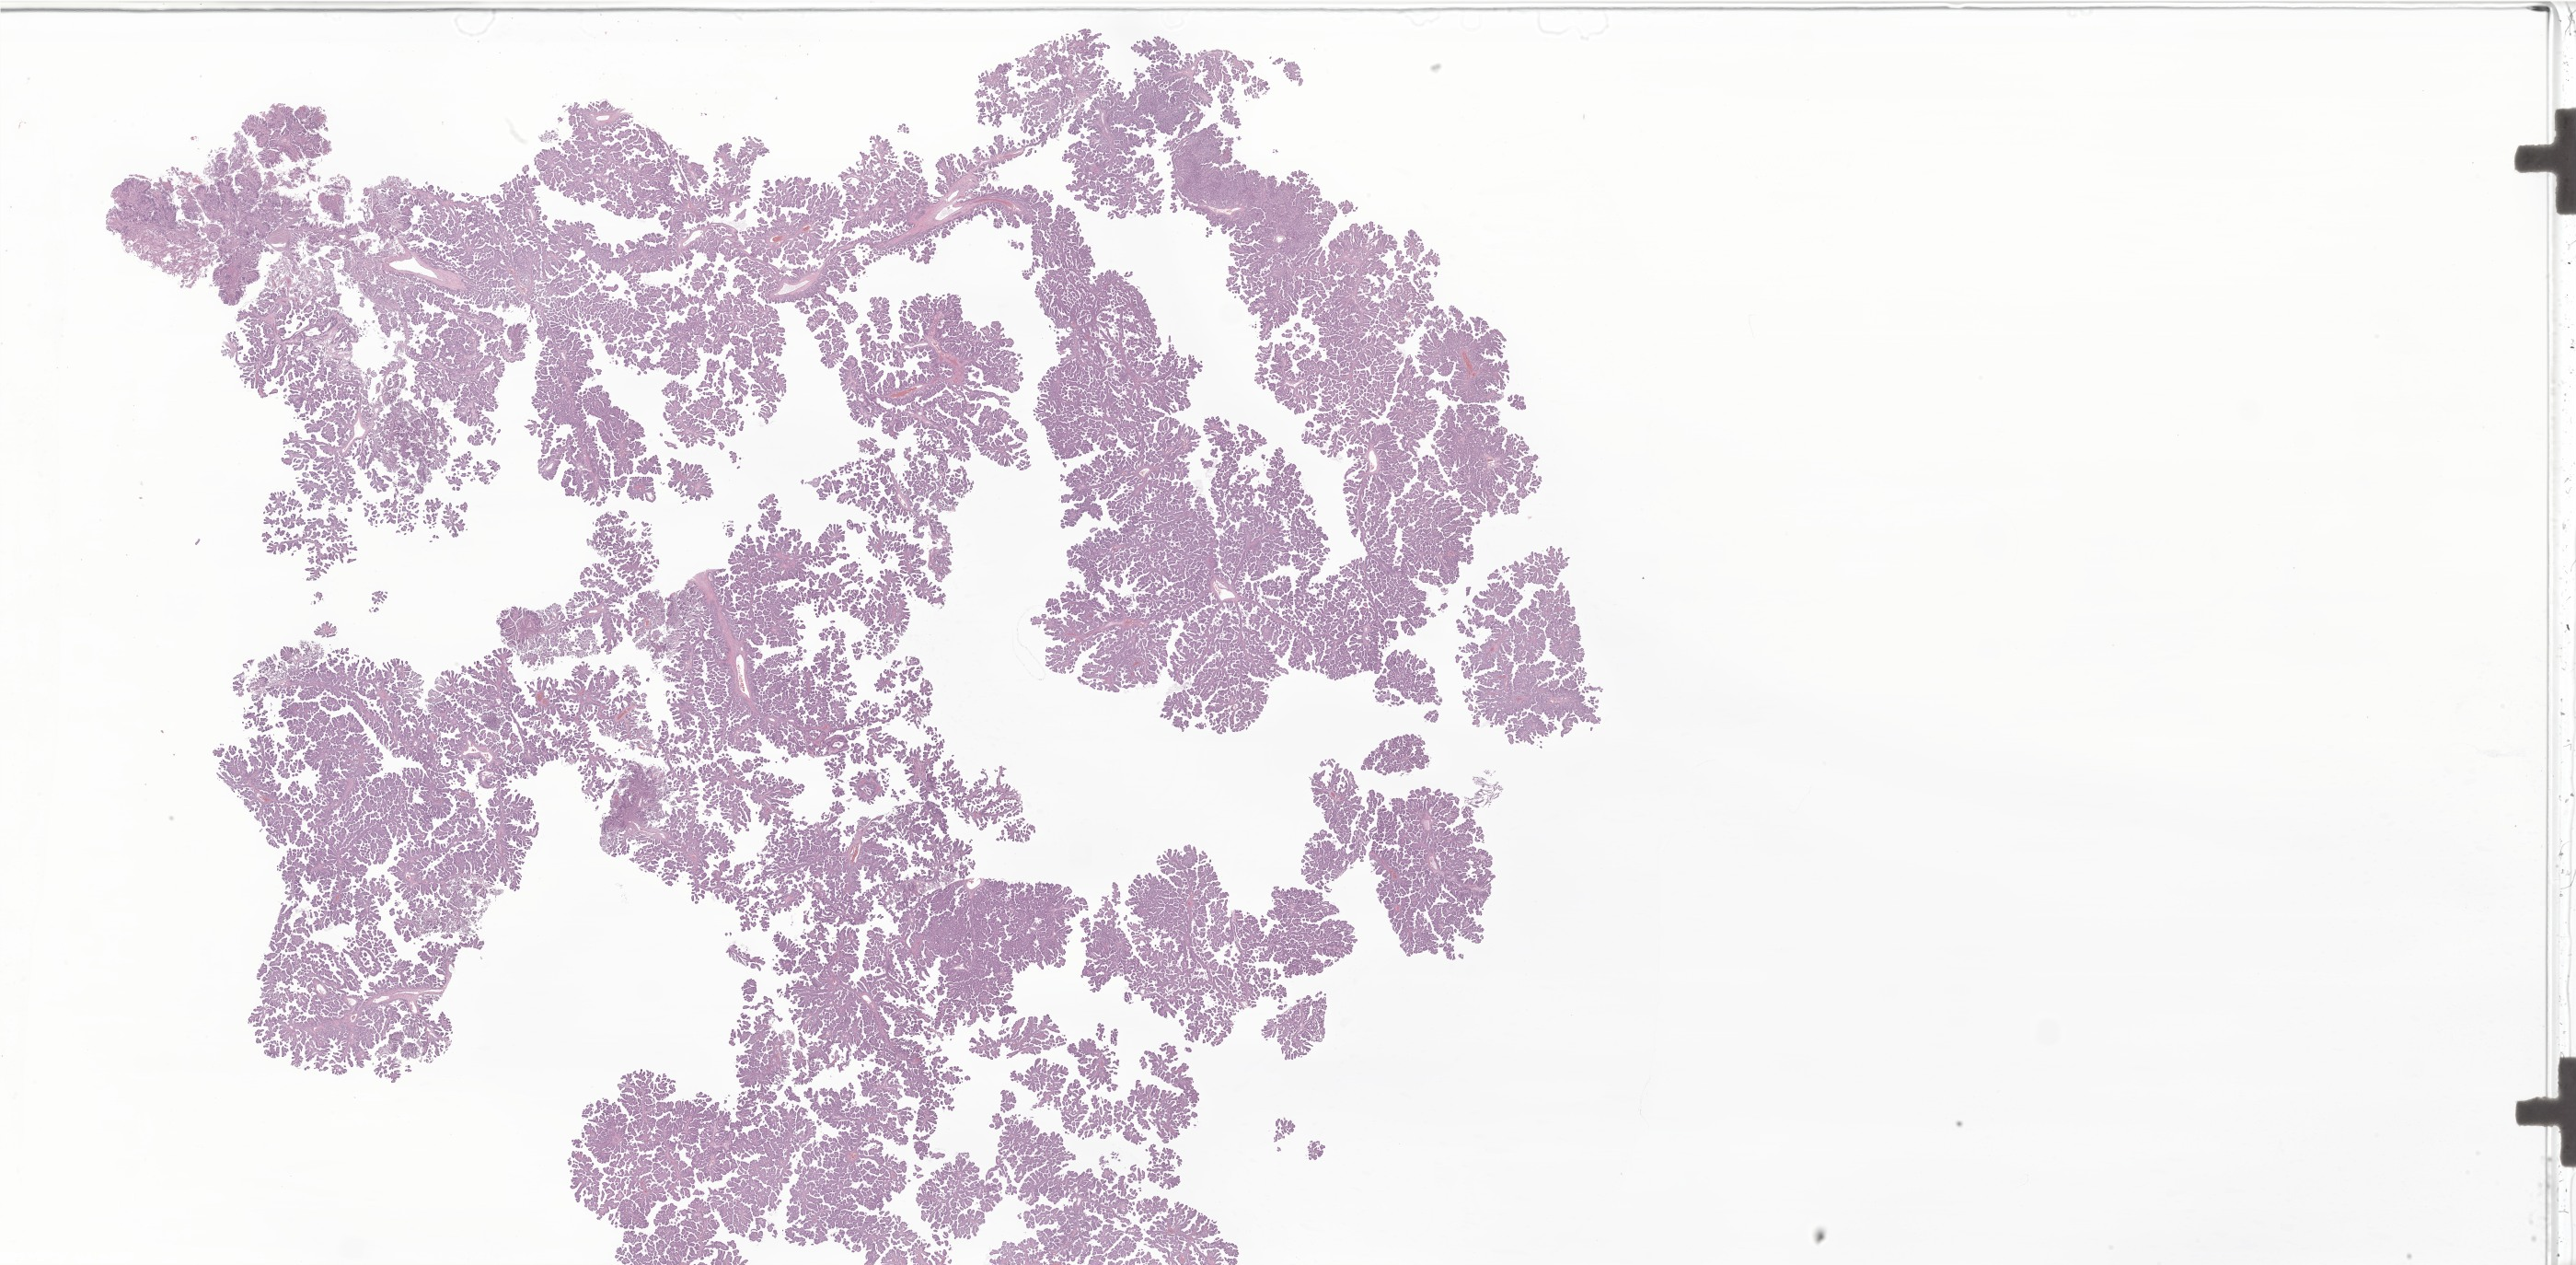
Digitized haematoxylin and eosin-stained section of tumor tissue from the brain, shown as a low-resolution overview of the whole scanned area (about 47.2 x 23.2 mm); formalin-fixed, paraffin-embedded (FFPE) tissue. Patient female; age 241 months.
Diagnosis (ICD-O-3 morphology term): Neoplasm, uncertain whether benign or malignant.